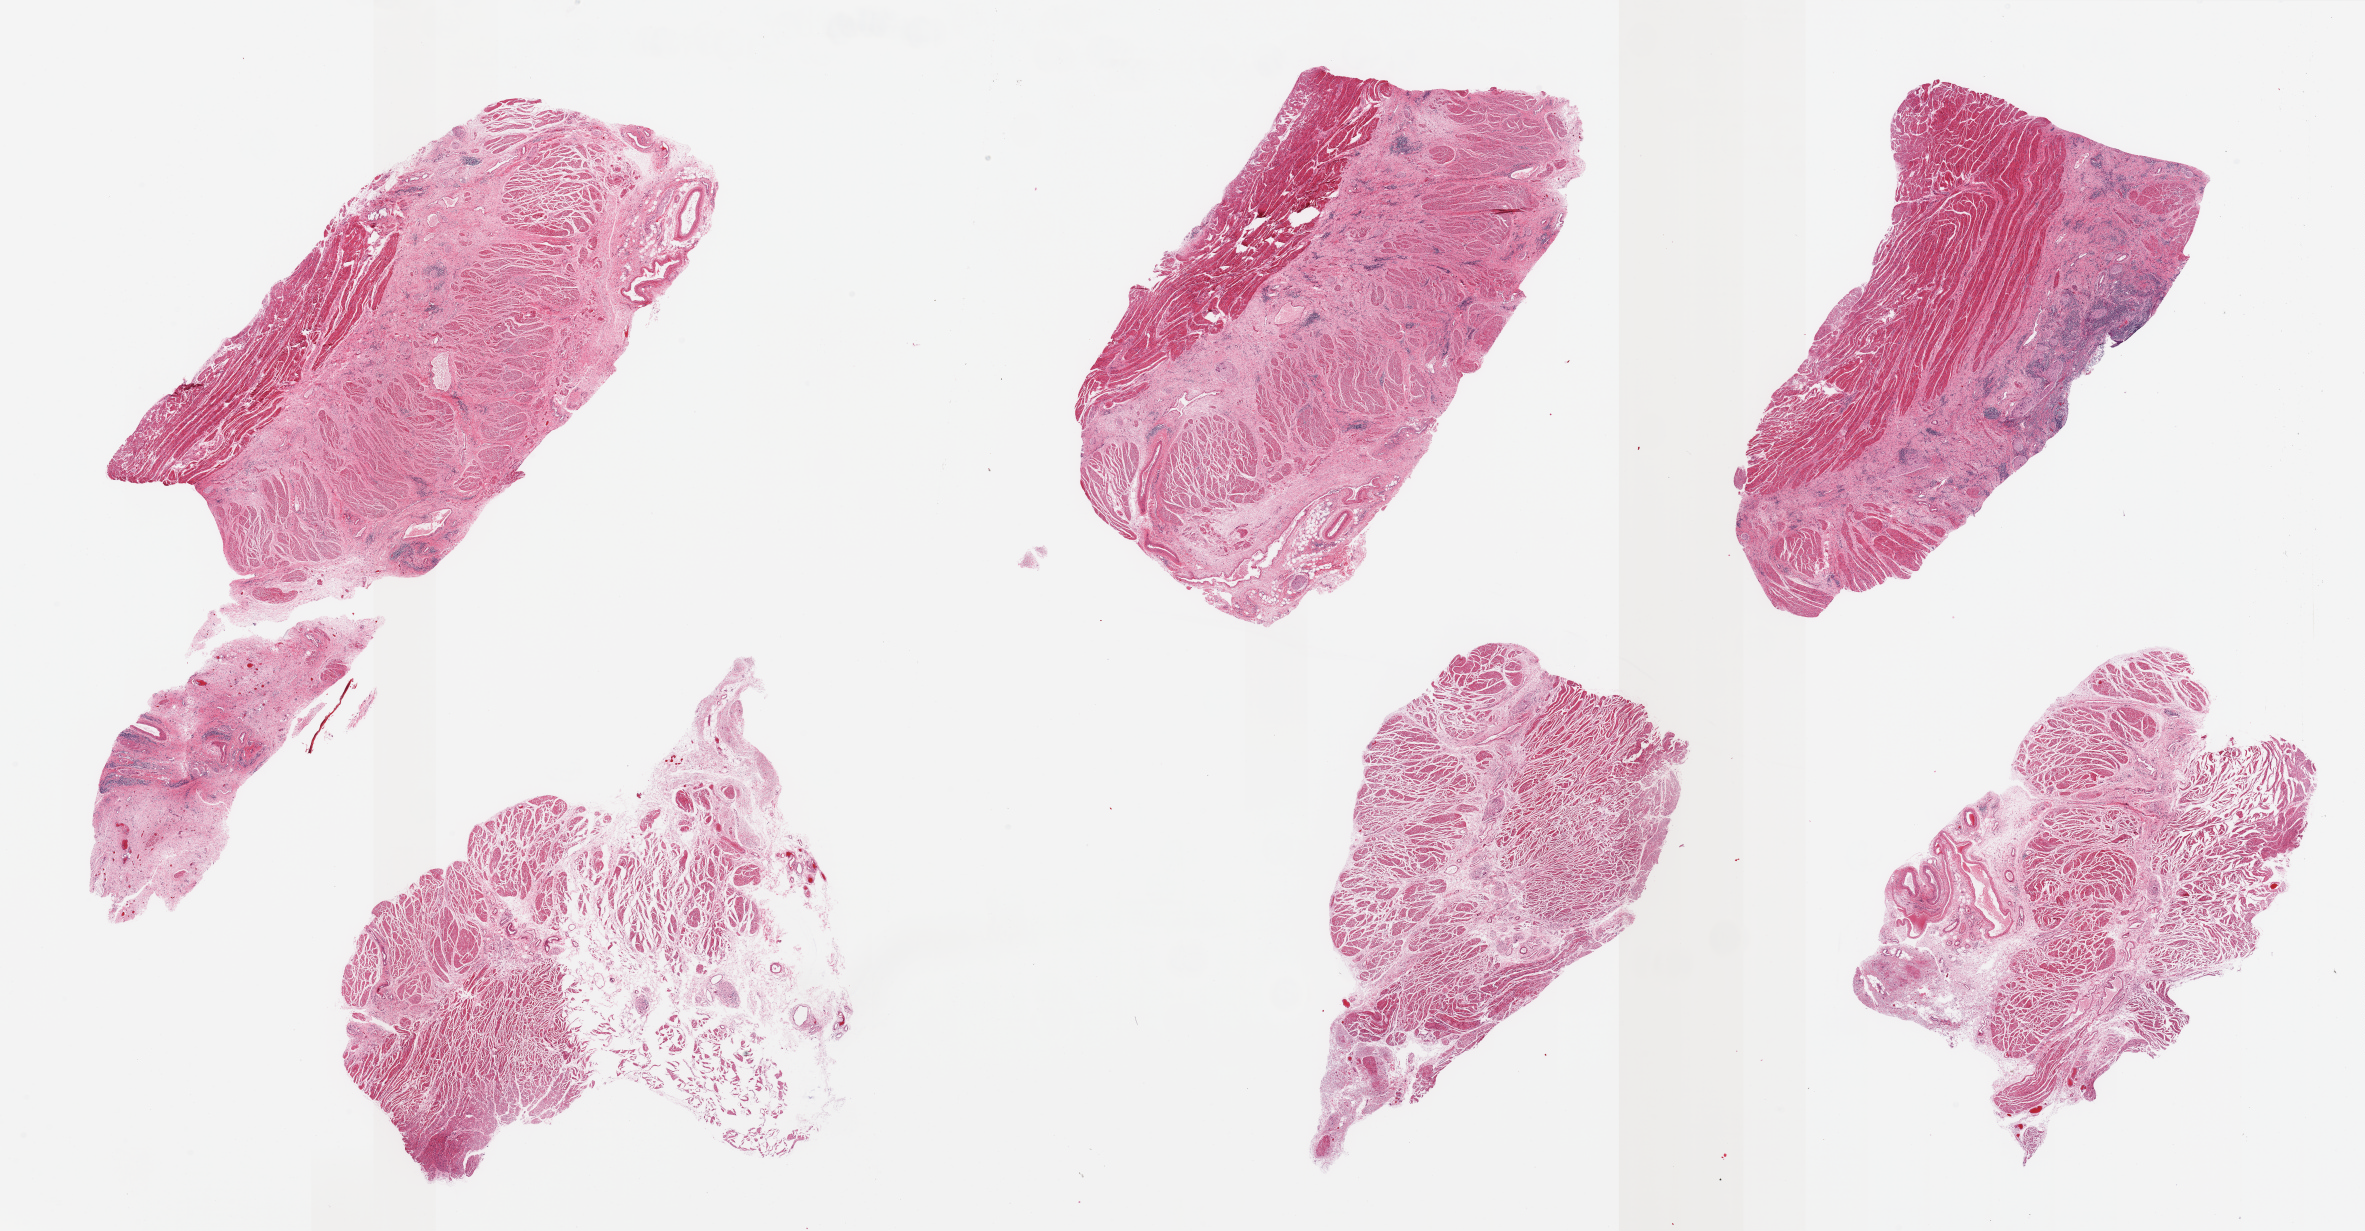
Digitized haematoxylin and eosin-stained section, brightfield — low-resolution overview of the scanned area, about 37.4 x 19.5 mm (from a 20x scan); PAXgene-fixed paraffin-embedded (PFPE) section; section of gastroesophageal junction (target tissue); donor tissue sample. Male donor.
- pathologist's review note for this sample: 6 pieces, ~30% target muscularis; majority is fibrotic serosa with chronic inflammation